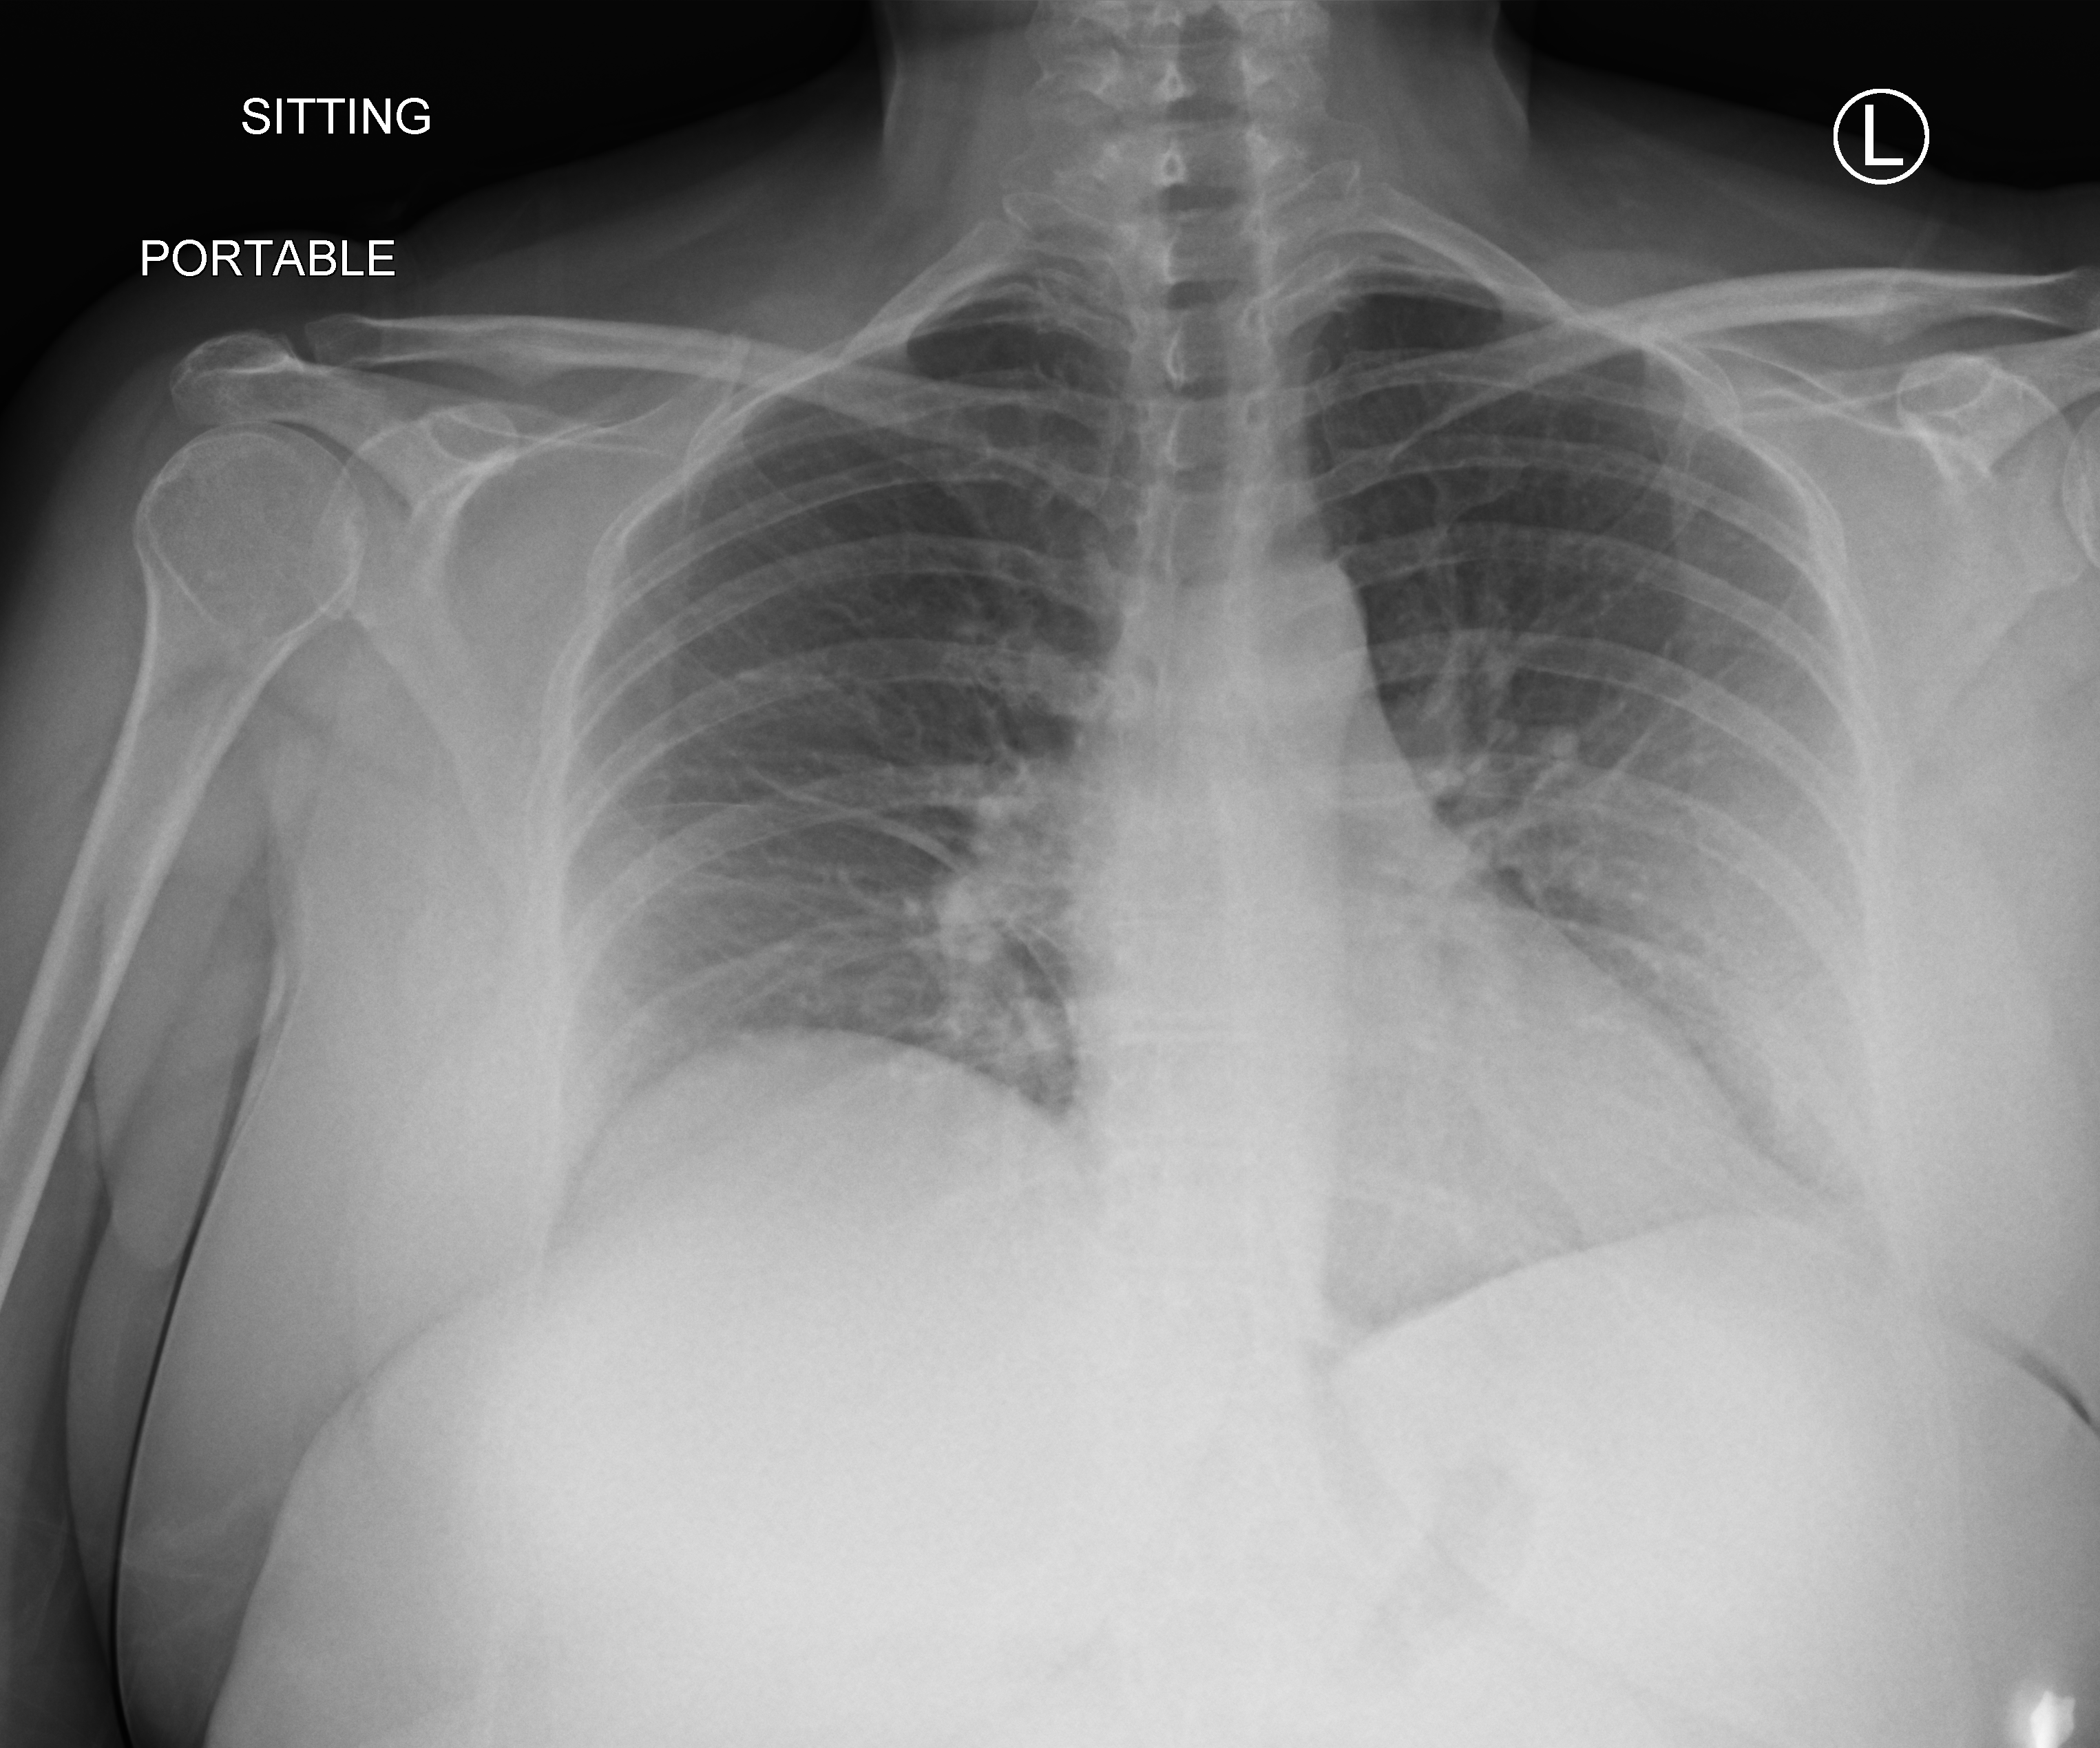
Bedside chest radiograph (computed radiography), anteroposterior (AP) projection. Female patient hospitalised with COVID-19, age 18–59 years.
Hospital-stay facts (about this admission, not read from this image; timing relative to this image not recorded): smoking status (admission record): never.